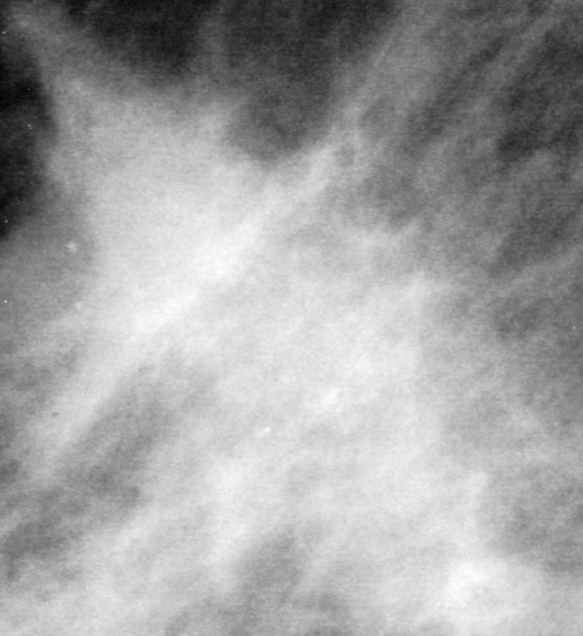
Cropped region of a digitized screen-film mammogram centred on a radiologist-marked abnormality, left breast, MLO view, BI-RADS breast density category 2 (scale 1–4).
Finding: mass, shape irregular, margins ill defined; BI-RADS assessment category 4; subtlety rating 4 on a 1 (subtle) to 5 (obvious) scale; pathology (as recorded): malignant.